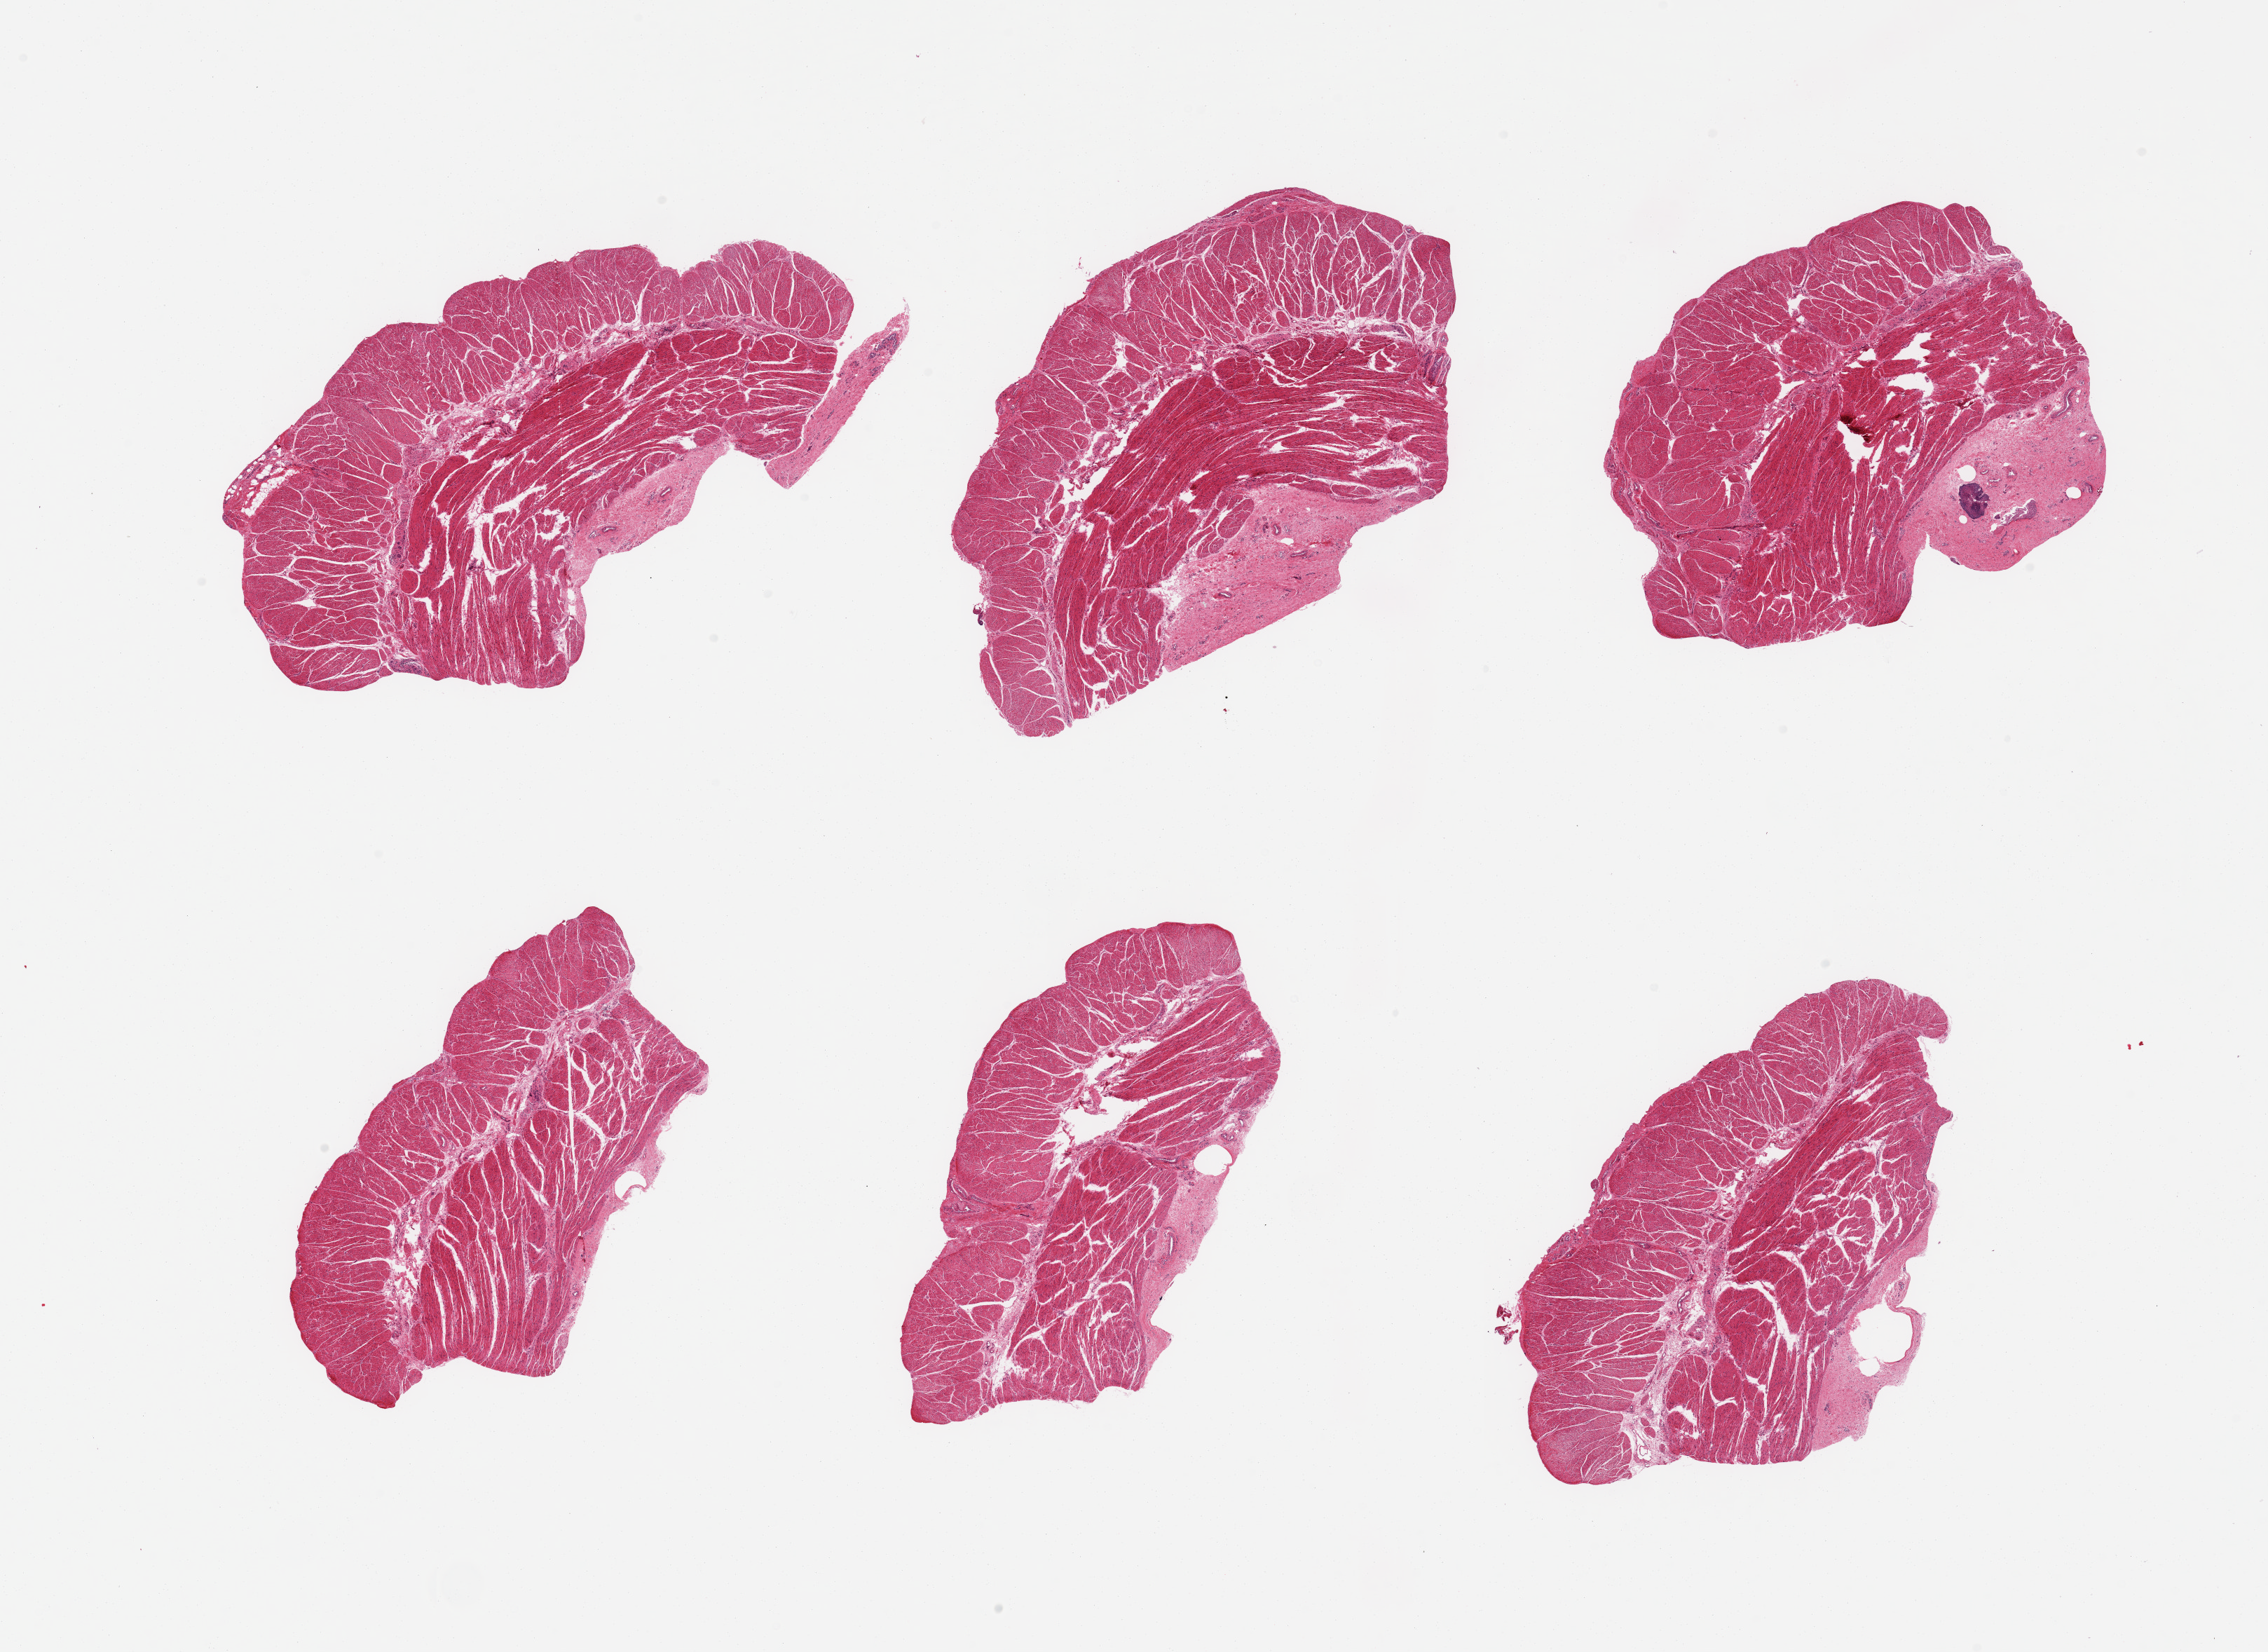
H&E whole-slide image, brightfield — whole scanned area (about 25.6 x 18.6 mm, from a 20x scan) shown as a low-resolution overview; PAXgene-fixed, paraffin-embedded tissue; target tissue: esophageal muscle; tissue donor sample. Donor: female.
- reviewer comment on this tissue sample: 6 pieces; well dissected muscularis except for a 0.4mm focus of epithelium in 1